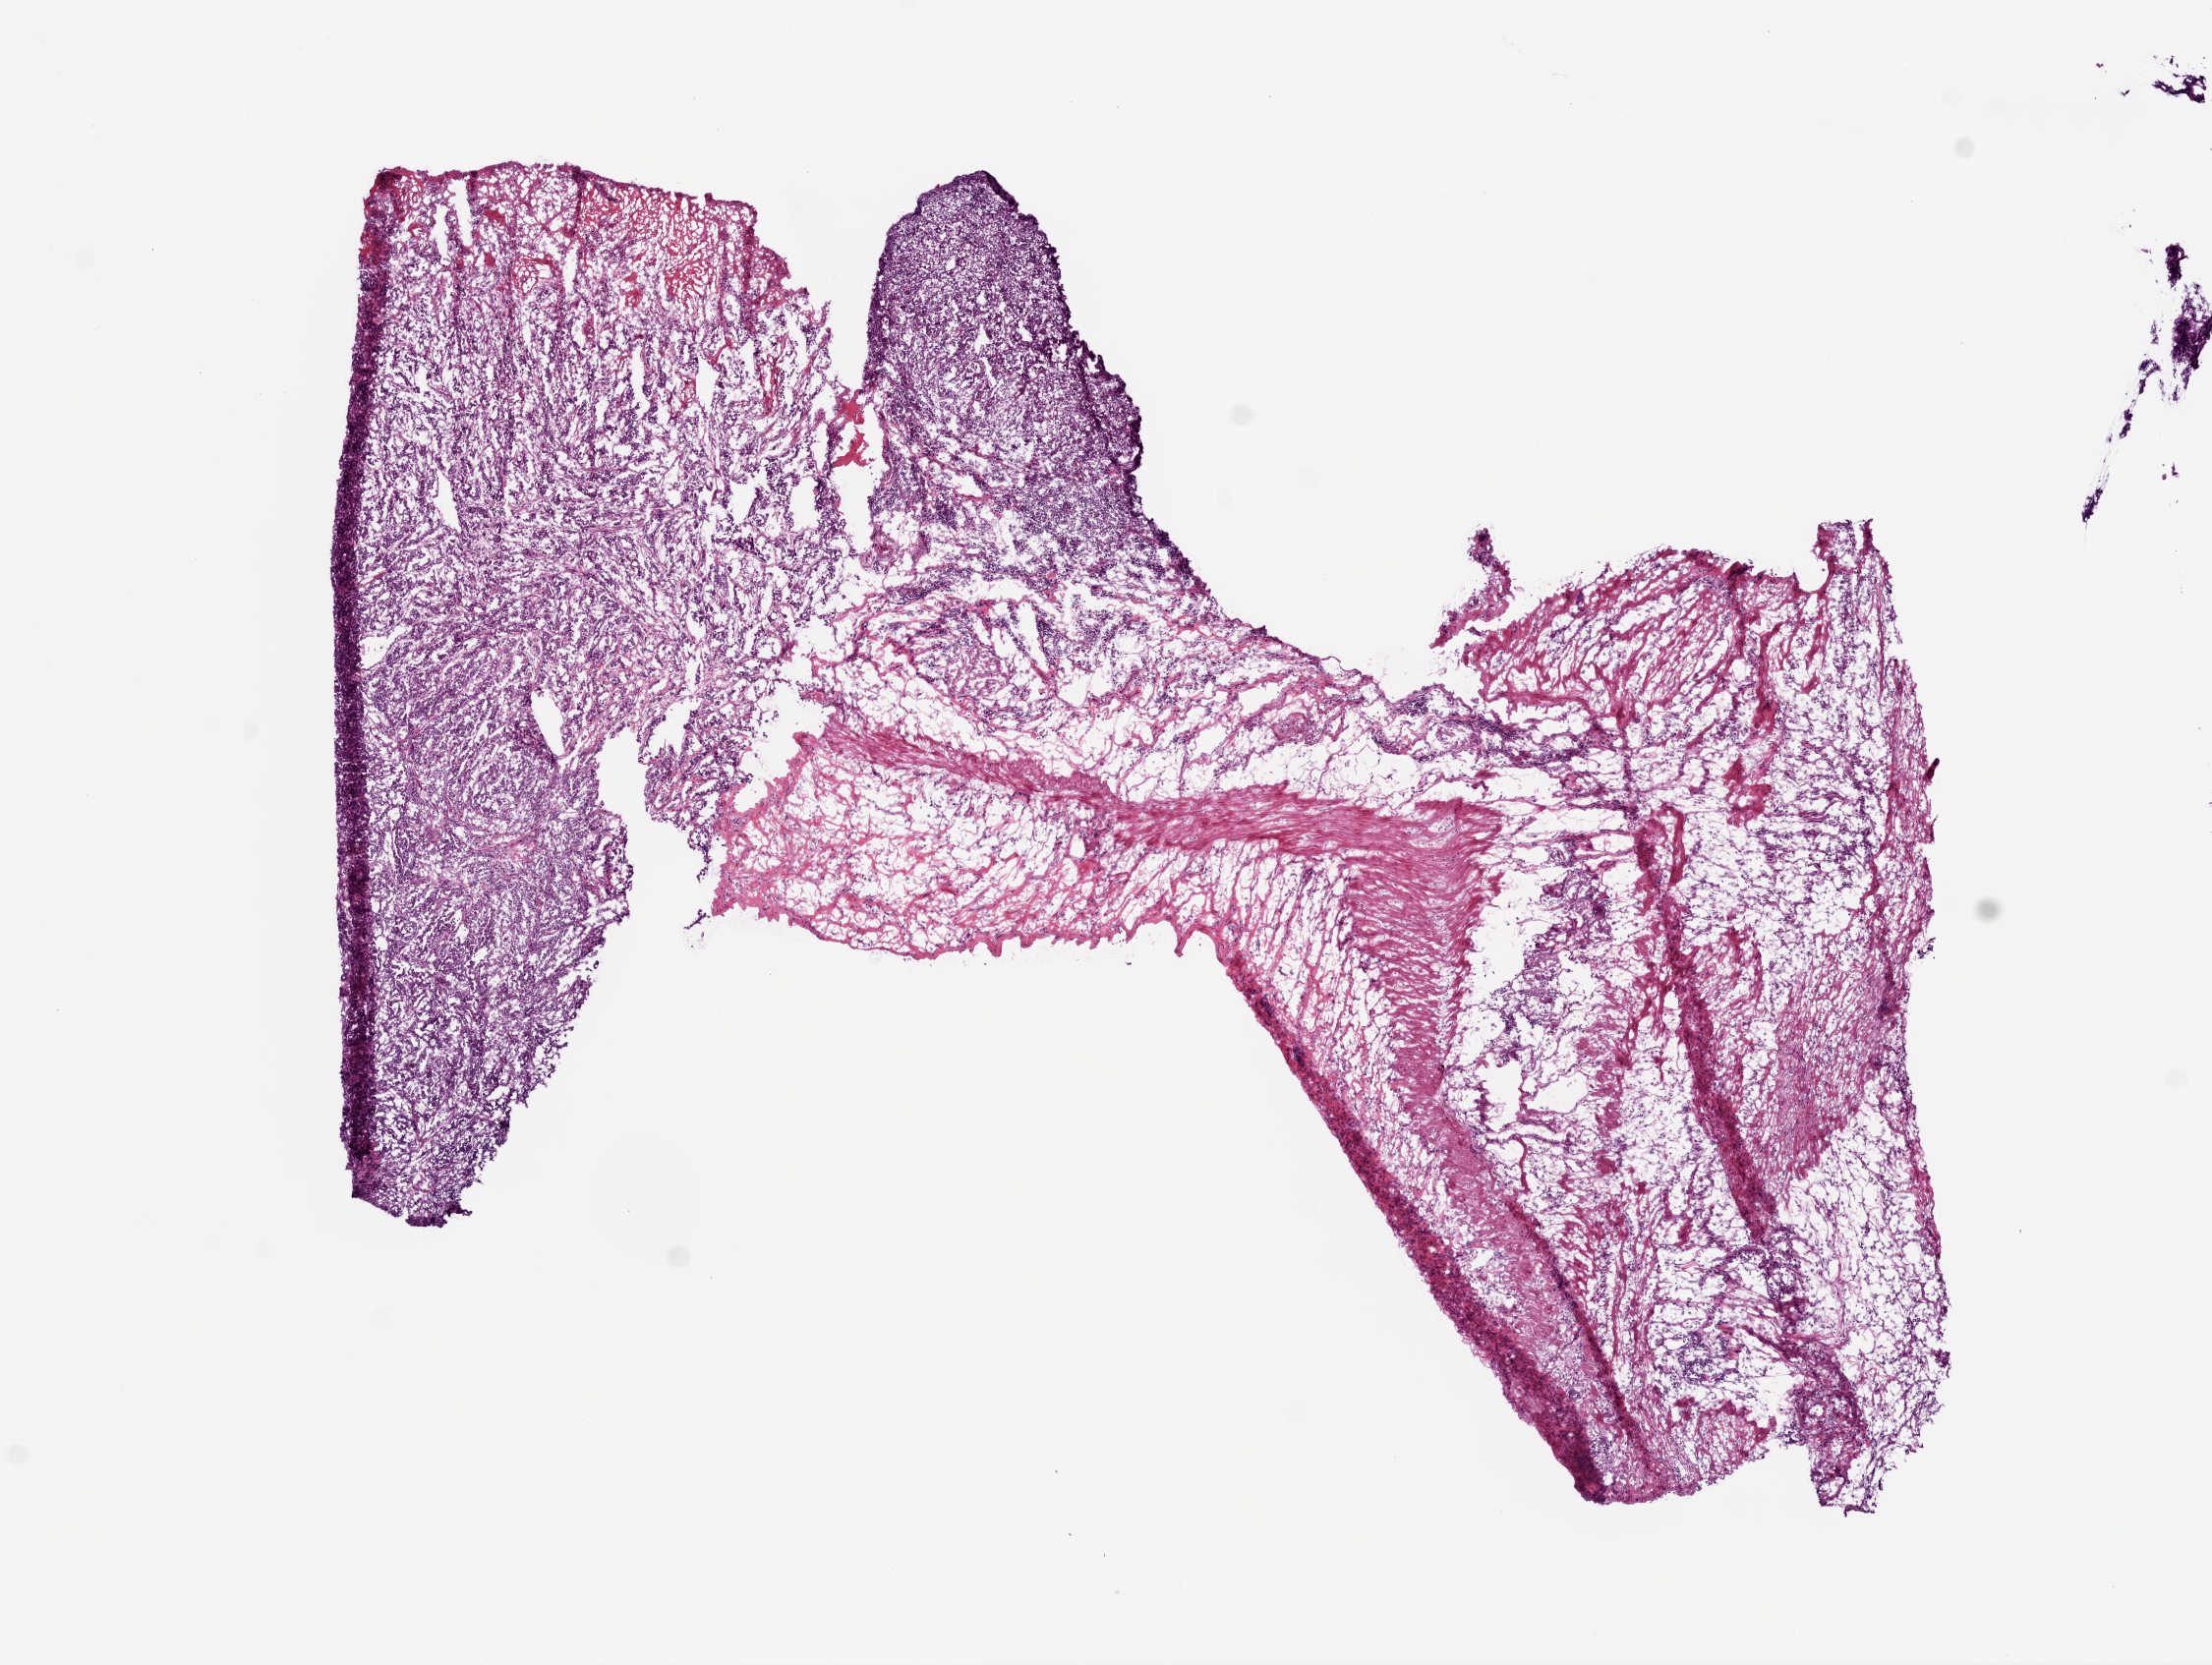
Whole-slide histology image, Hematoxylin and eosin (H&E) stained, whole scanned area (about 9.0 x 6.8 mm, slide scanned at 20x) shown as a low-resolution overview. Frozen section from the top of the tissue portion. Stomach, primary tumour sample. Patient sex: male. Histologic grade: G3 (poorly differentiated). Slide review estimates, as recorded: tumour cells 50%, tumour nuclei 75%, normal cells 0%, stromal cells 50%, necrosis 0%.
- pathologic diagnosis: Adenocarcinoma, NOS (cardia, NOS)
- AJCC pathologic stage: II (5th edition)
- lymph nodes positive (case pathology): 1 of 31 examined